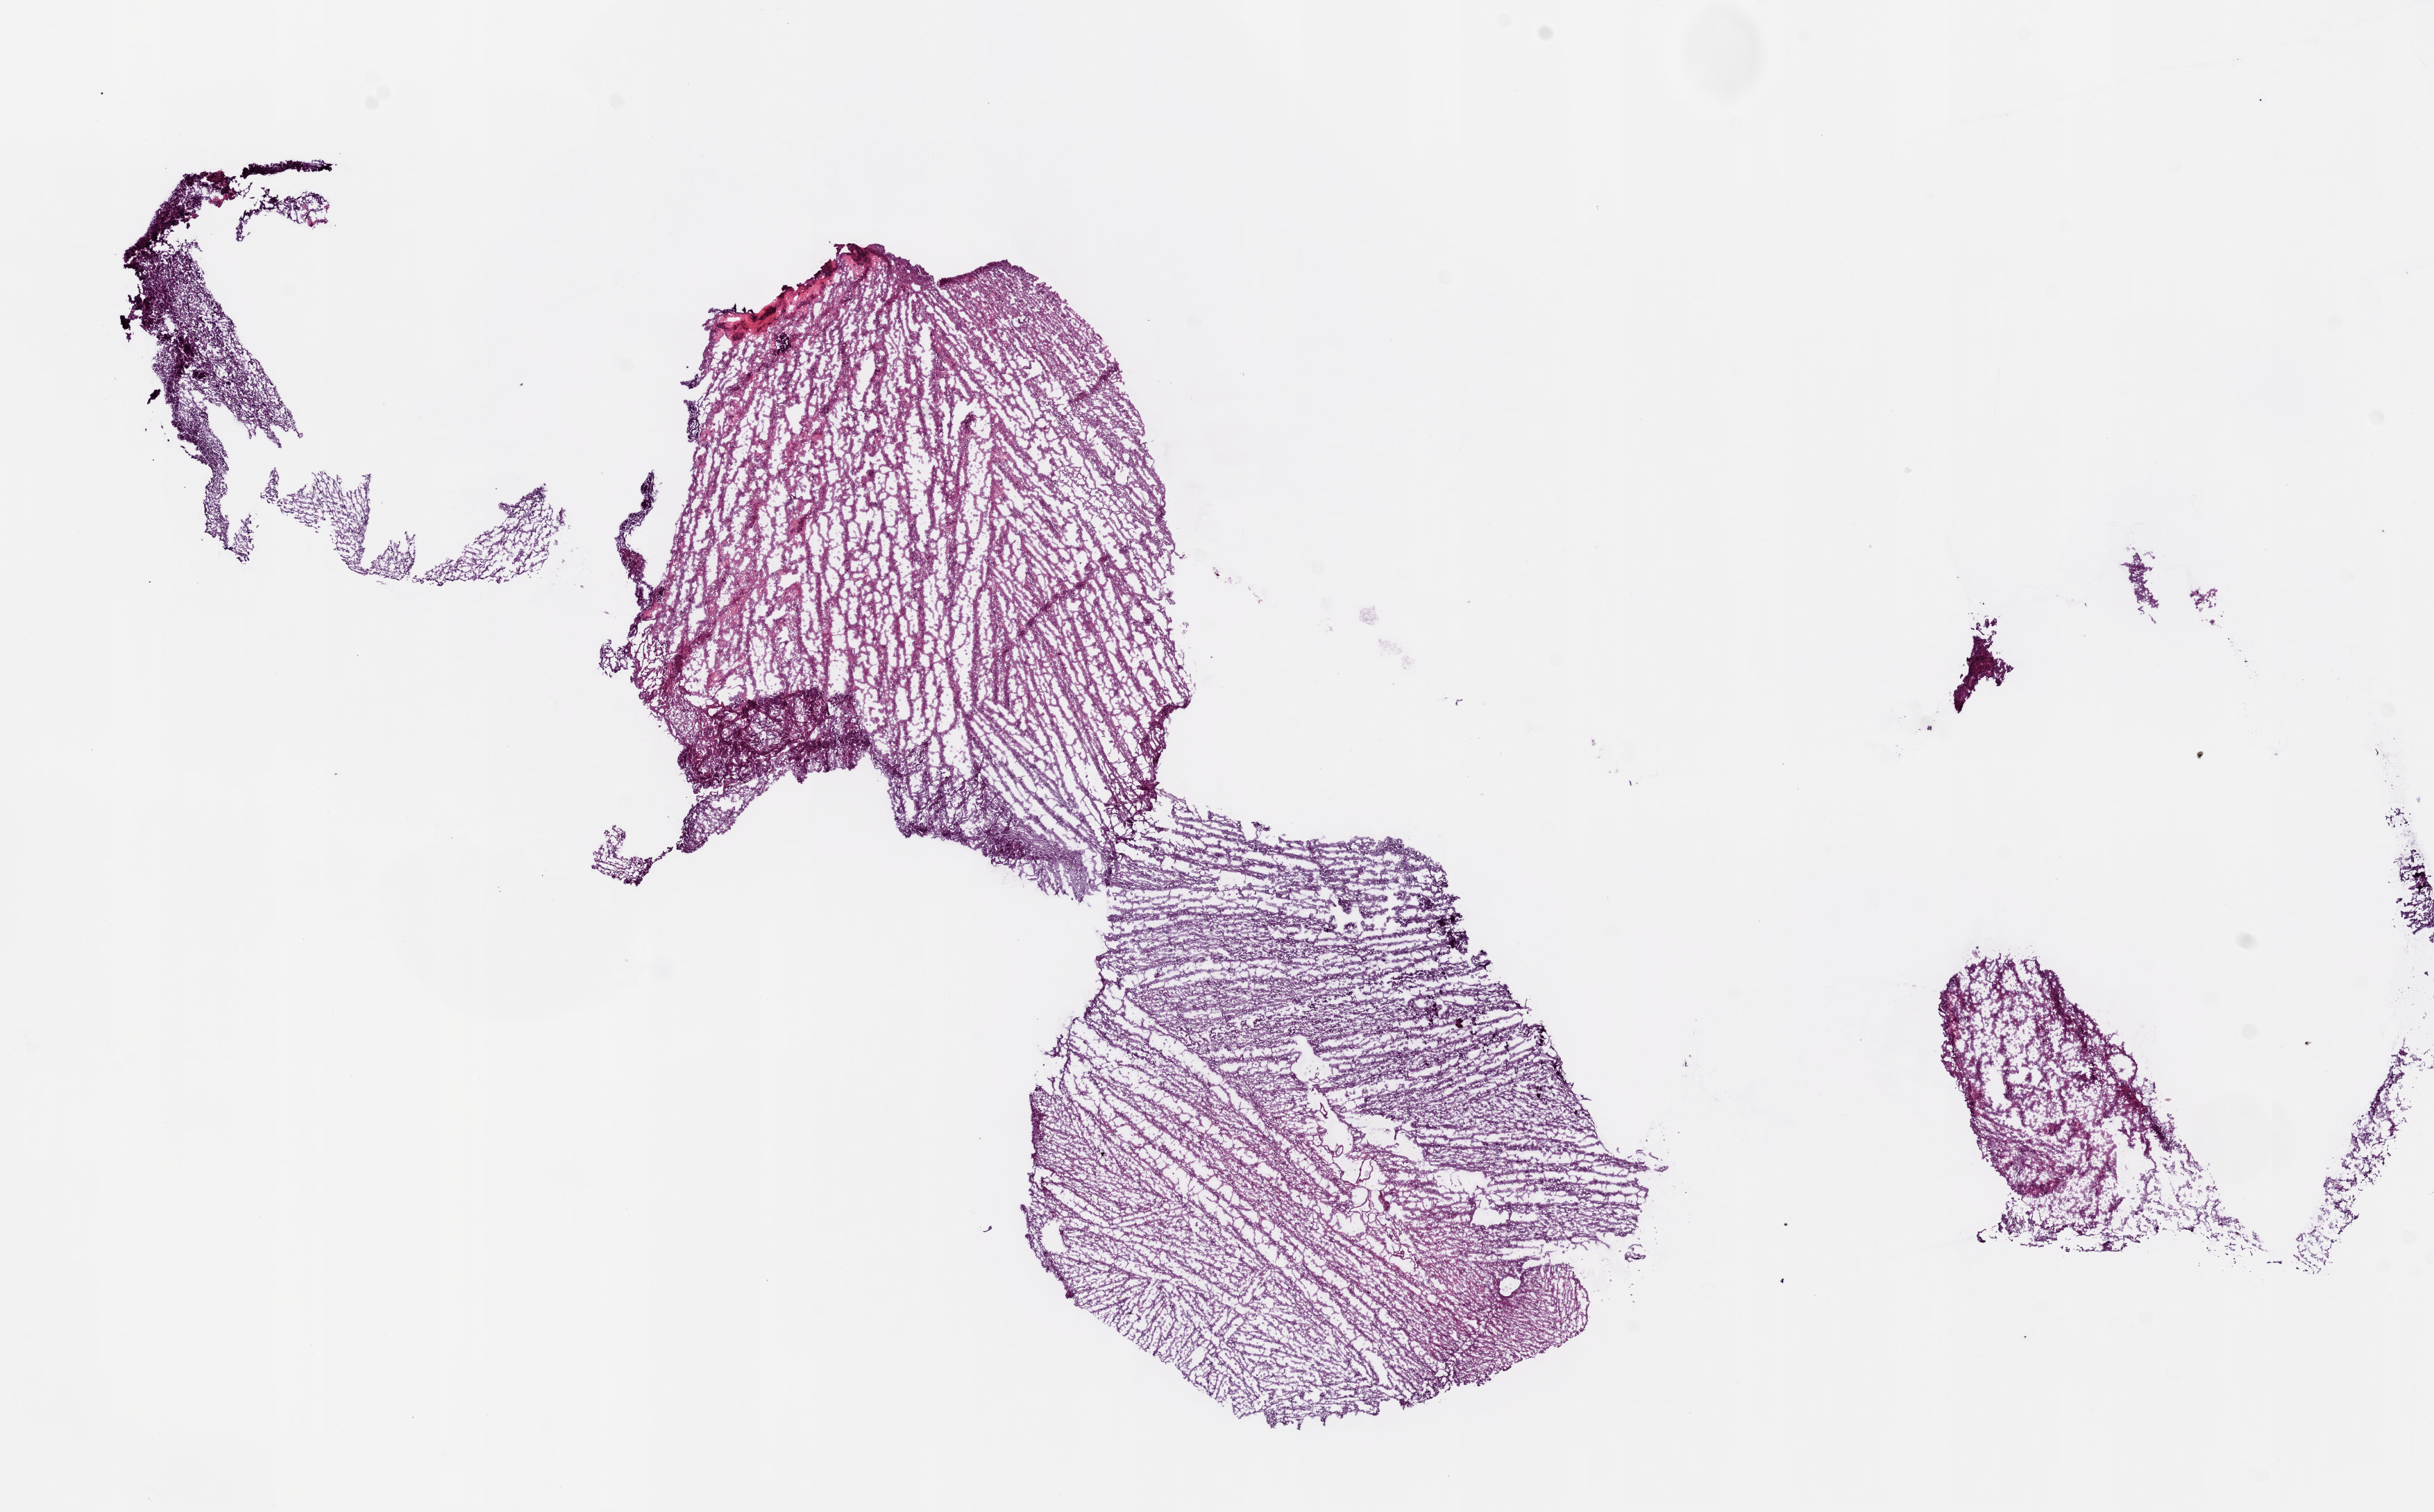
Digitized H&E tissue section (whole slide) — low-resolution overview of the scanned area, about 14.1 x 8.7 mm. Frozen section from the bottom of the tissue portion. Primary tumour sample from the brain. Female patient; age at initial diagnosis 47 years. Composition of this section per pathologist review: tumour cells 100%, tumour nuclei 75%.
Histologic diagnosis: Oligodendroglioma, NOS.